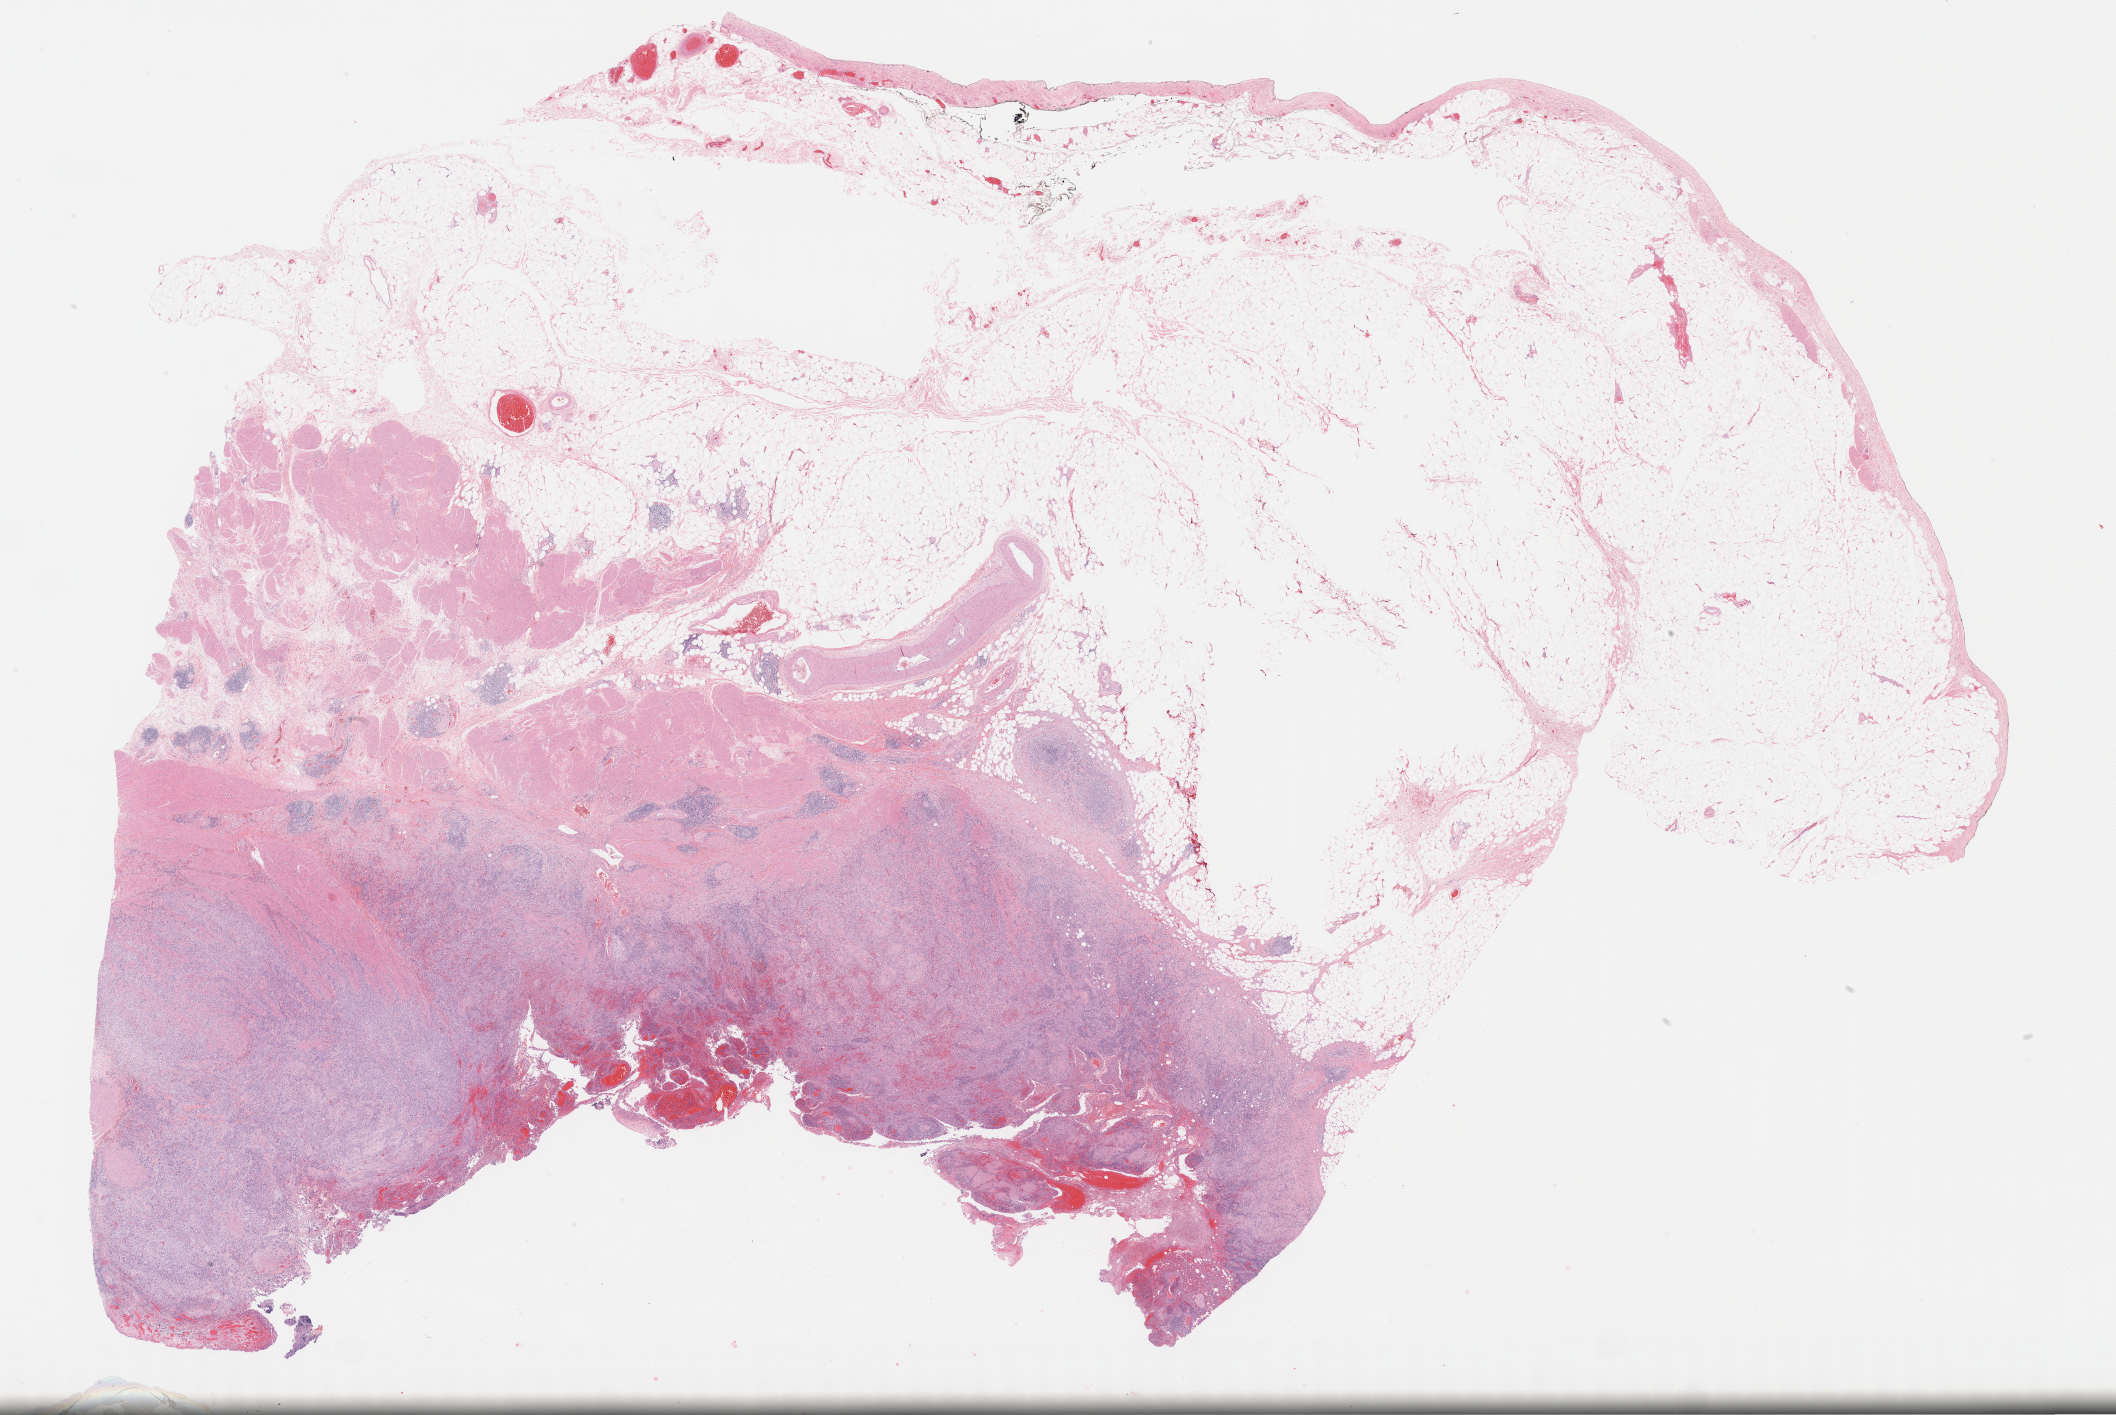
Whole-slide histology image, Hematoxylin and eosin (H&E) stained, shown as a low-resolution overview of the whole scanned area (about 34.2 x 22.9 mm), formalin-fixed paraffin-embedded (FFPE) diagnostic section, sample: primary tumour, bladder. Patient: male, age at initial diagnosis 48 years. Histologic grade: high grade.
* pathologic diagnosis: Transitional cell carcinoma (lateral wall of bladder)
* AJCC pathologic stage: III